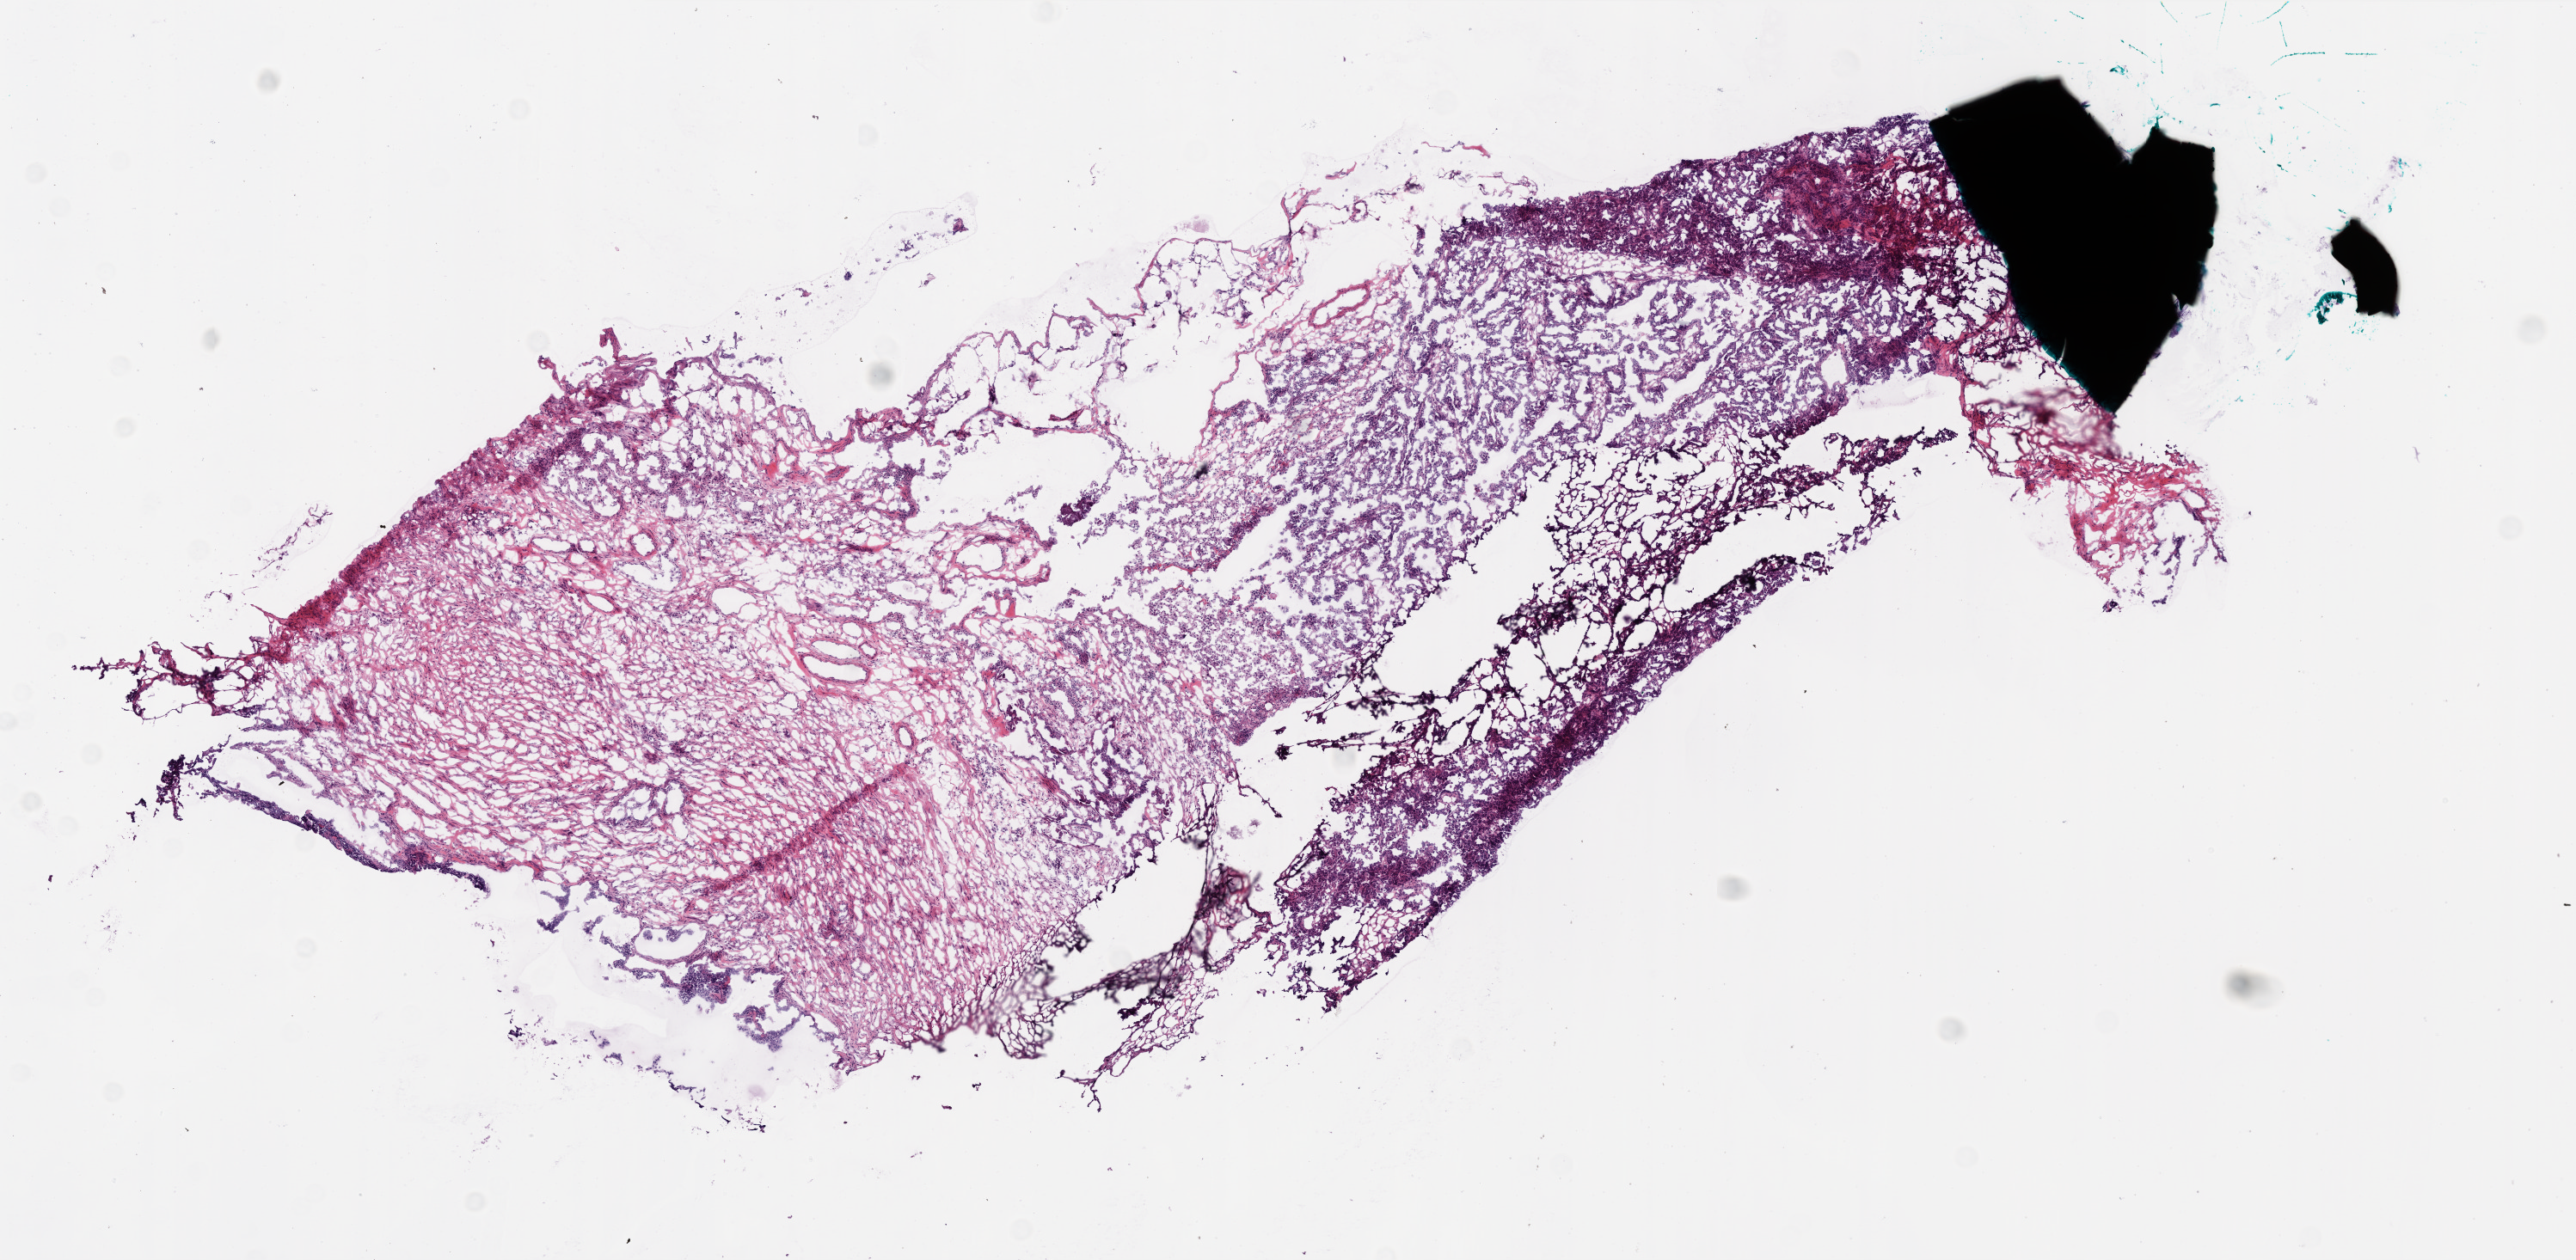
Digitized Hematoxylin and eosin (H&E) stained tissue section (whole slide), shown as a low-resolution overview of the whole scanned area (about 12.0 x 5.9 mm, acquisition: 20x scan). Frozen section from the bottom of the tissue portion. Primary tumour sample from the ovary. Female, age 53 years at initial diagnosis. Histologic grade: G3 (poorly differentiated). Slide review estimates, as recorded: tumour nuclei 80%, normal cells 0%, necrosis 1%.
- histologic diagnosis: Serous cystadenocarcinoma, NOS
- FIGO stage: IIIC